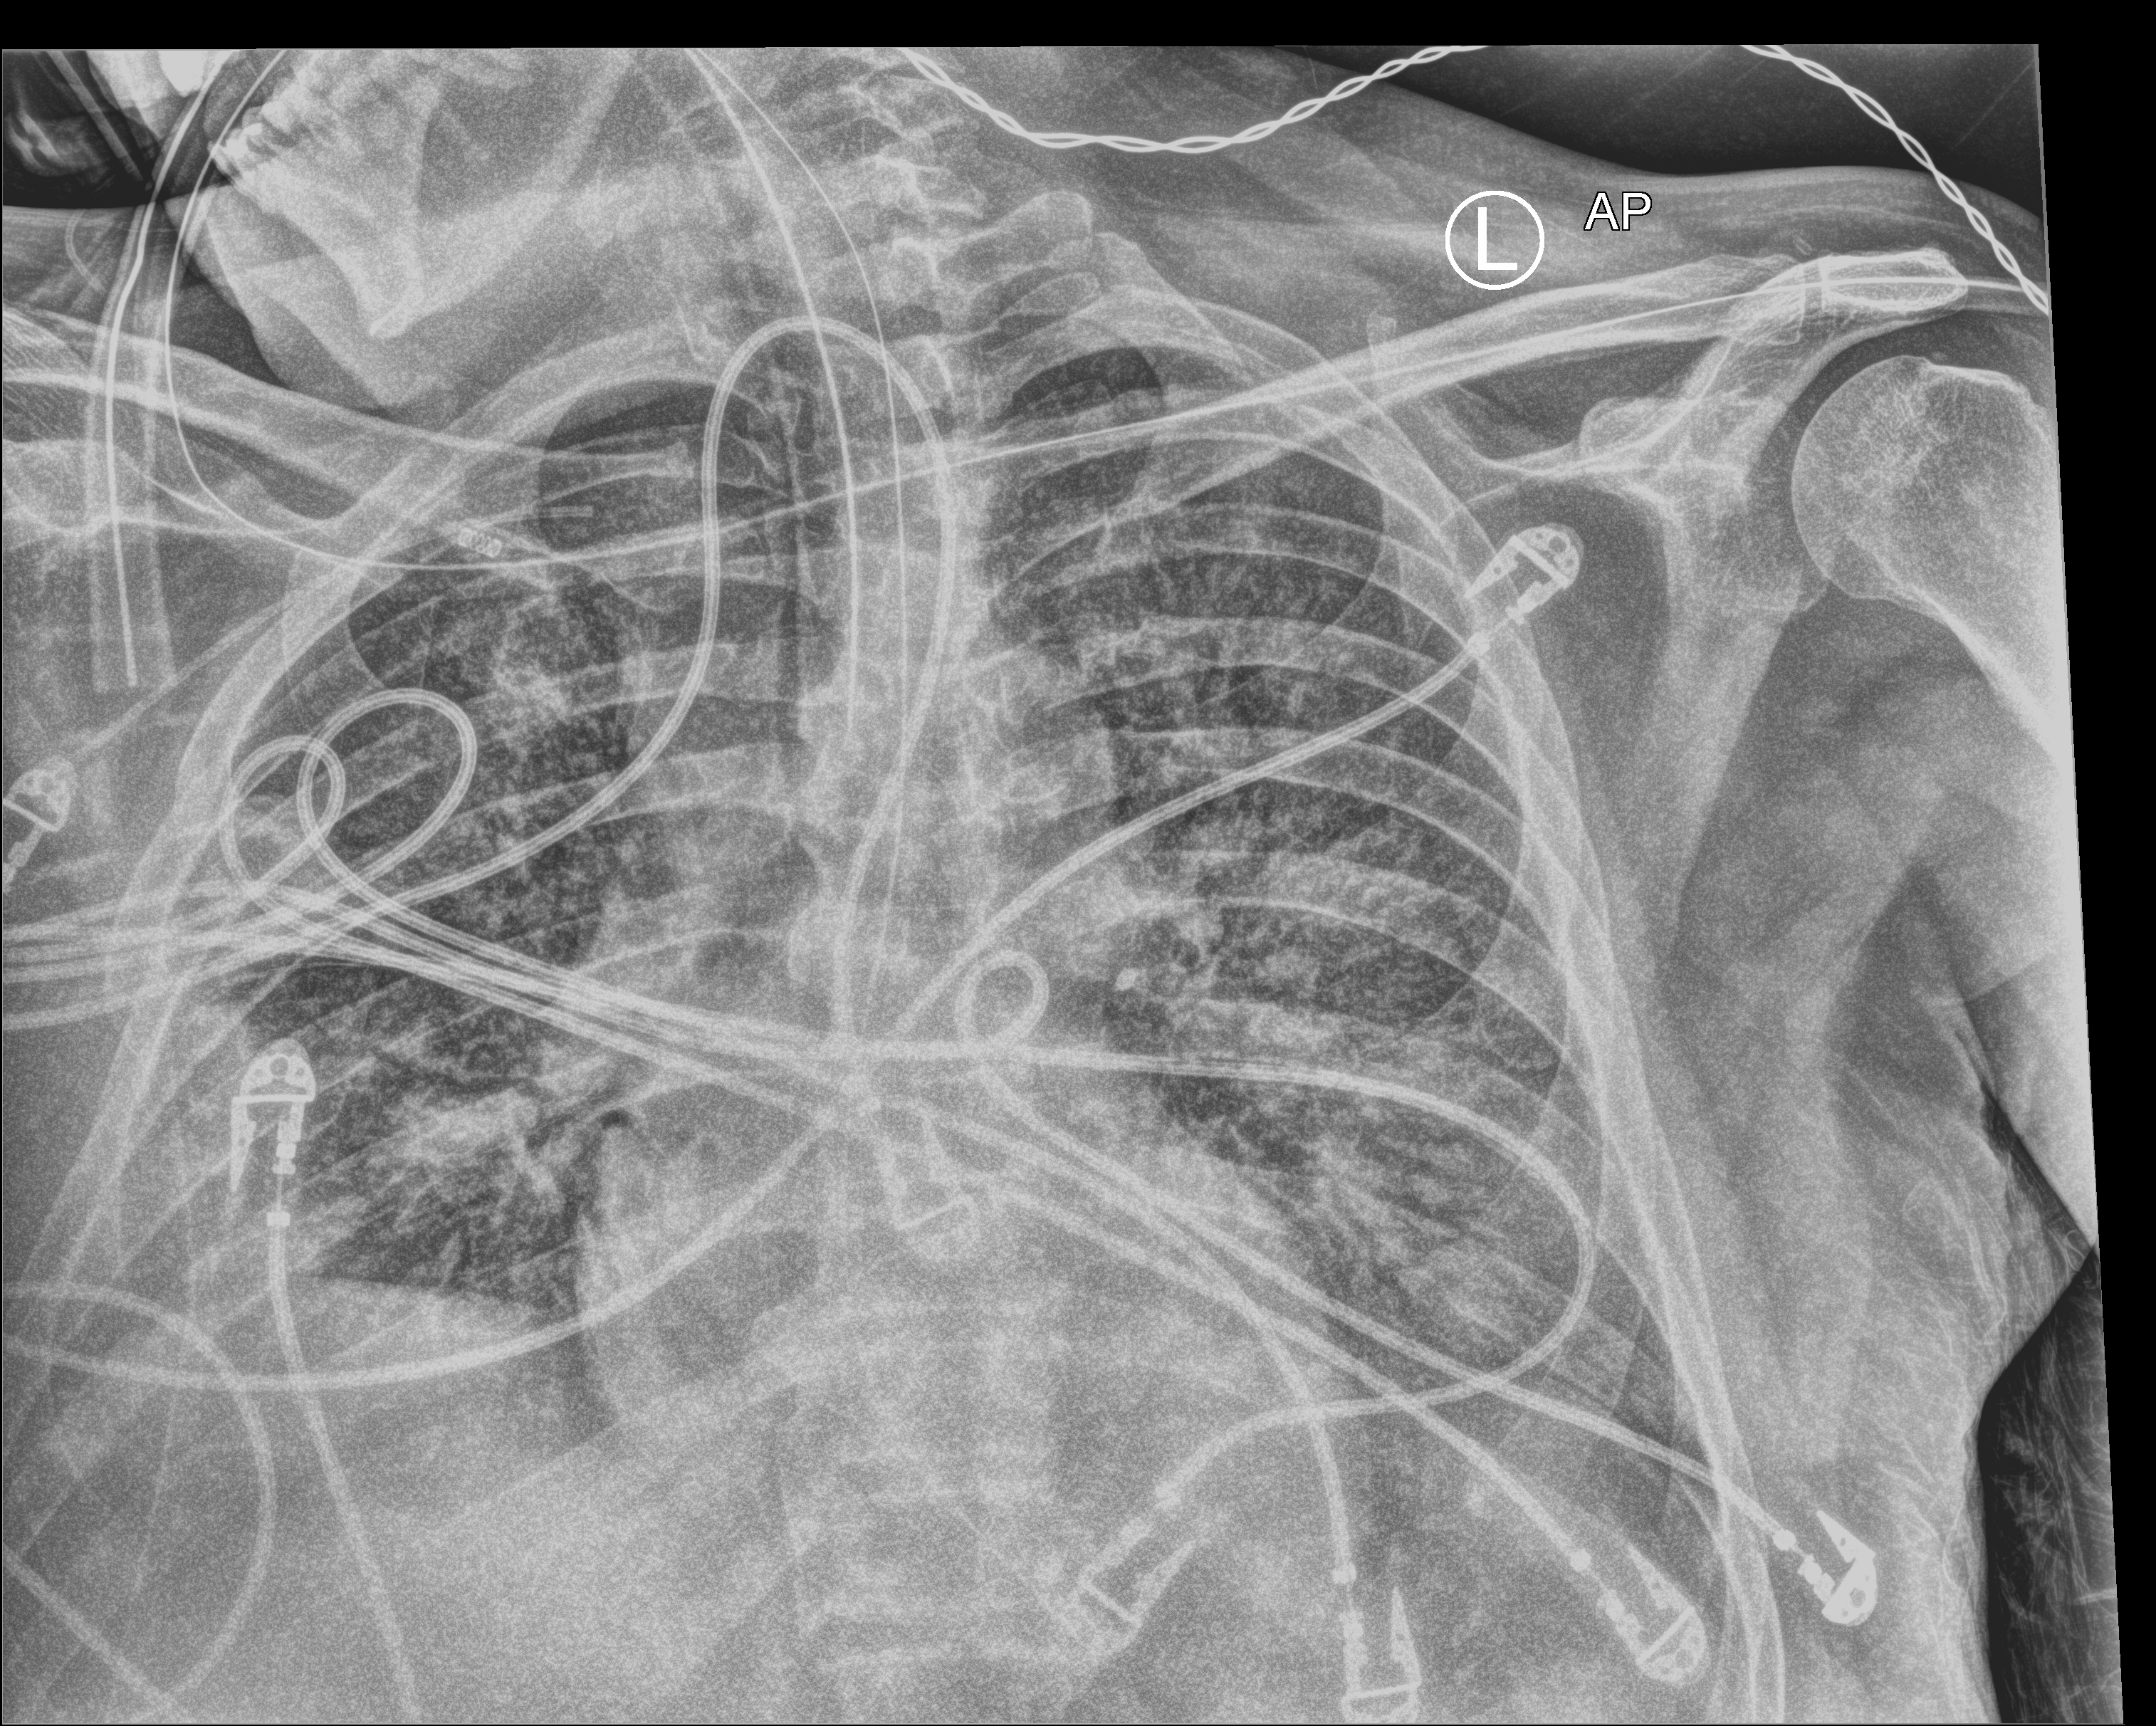
Chest X-ray (portable); anteroposterior (AP) projection. Patient hospitalised with COVID-19; male, aged 60–74 years.
Hospital-stay facts (about this admission, not read from this image; timing relative to this image not recorded): admitted to intensive care during this hospital stay: yes; COPD (admission record): no; length of hospital stay: 15 days.